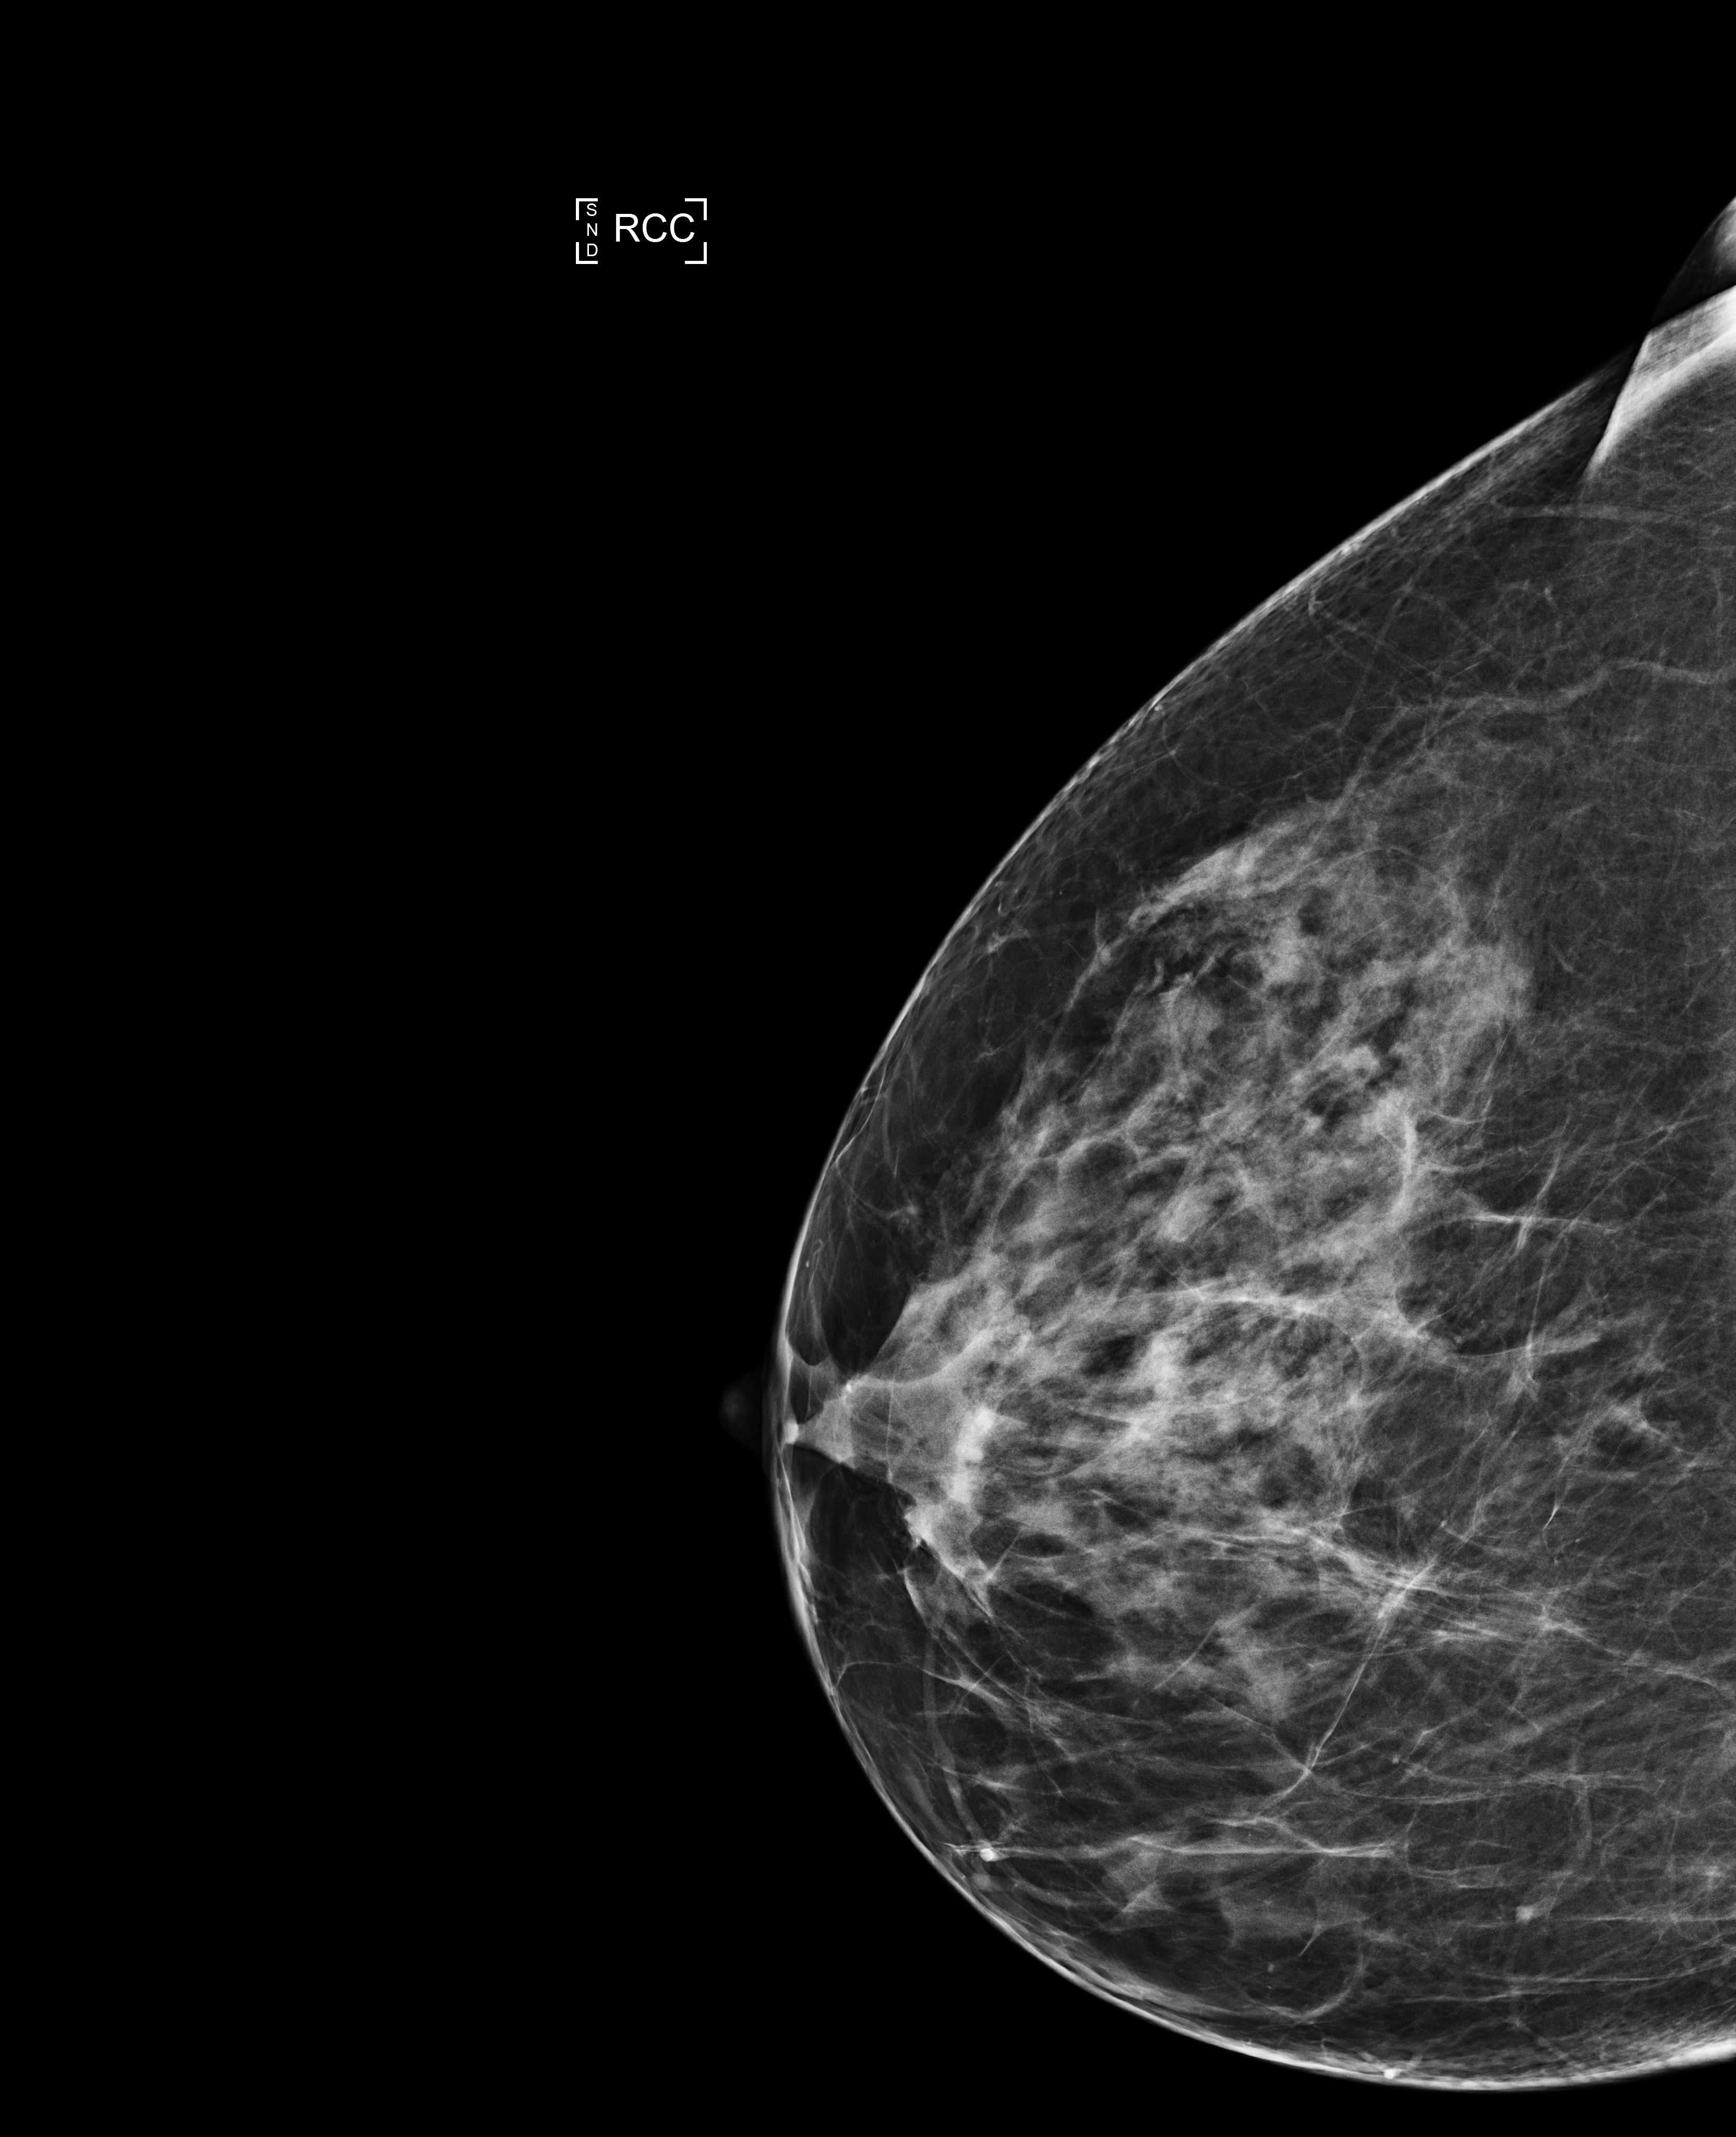
Screening examination, compressed breast thickness 54 mm, system: Selenia Dimensions. Patient: female, 54 years.
Image type: full-field digital mammogram. Breast: right. Projection: craniocaudal (CC) view.